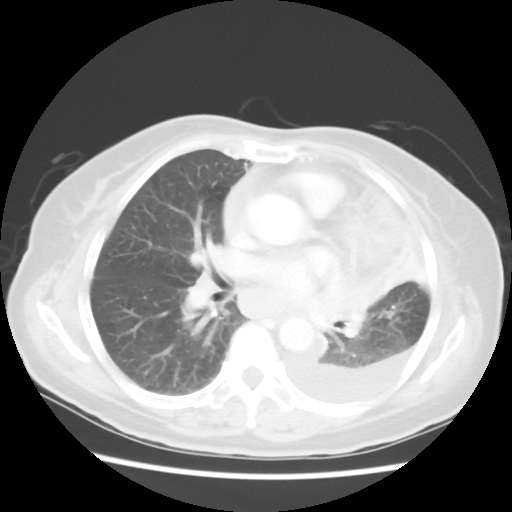
Chest CT, one axial slice; position 29 of 52 along the scan axis; lung window (W 1500 / L -600 HU); 5 mm slice thickness; 512 × 512 image matrix. Female patient, age 72 years. From the clinical record (not read from this slice): clinical TNM (as recorded): T4 N3 M1b.
Annotated regions visible in this slice (bounding box drawn by a radiologist):
- lung tumour (recorded histology: large cell carcinoma): bounding box [x1, y1, x2, y2] px = [323, 275, 387, 334]